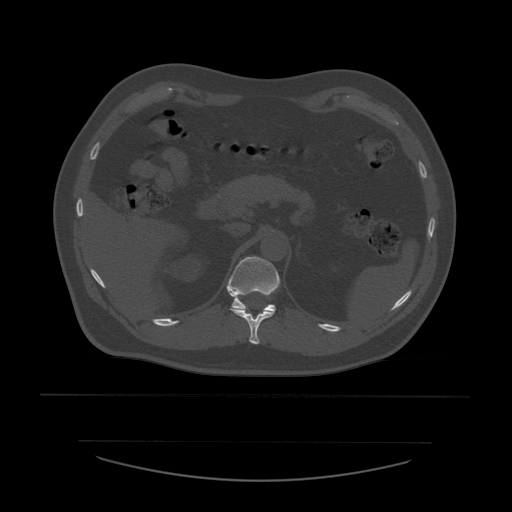
CT including the spine, one axial slice. Slice 263 of 532 in the series (ordered by position). 120 kVp. Bone window (W 1800 / L 400 HU). 1.25 mm slice thickness. 512 × 512 image matrix. Patient age 44 years. Case-level facts recorded for this patient, not image findings: primary cancer: soft tissue sarcoma.
Outlined on this slice (semi-automatic segmentation, software-assisted and operator-edited):
- T11 vertebra: bounding box <230,308,275,345> (left, top, right, bottom; pixels)
- T12 vertebra: <227,257,280,312>